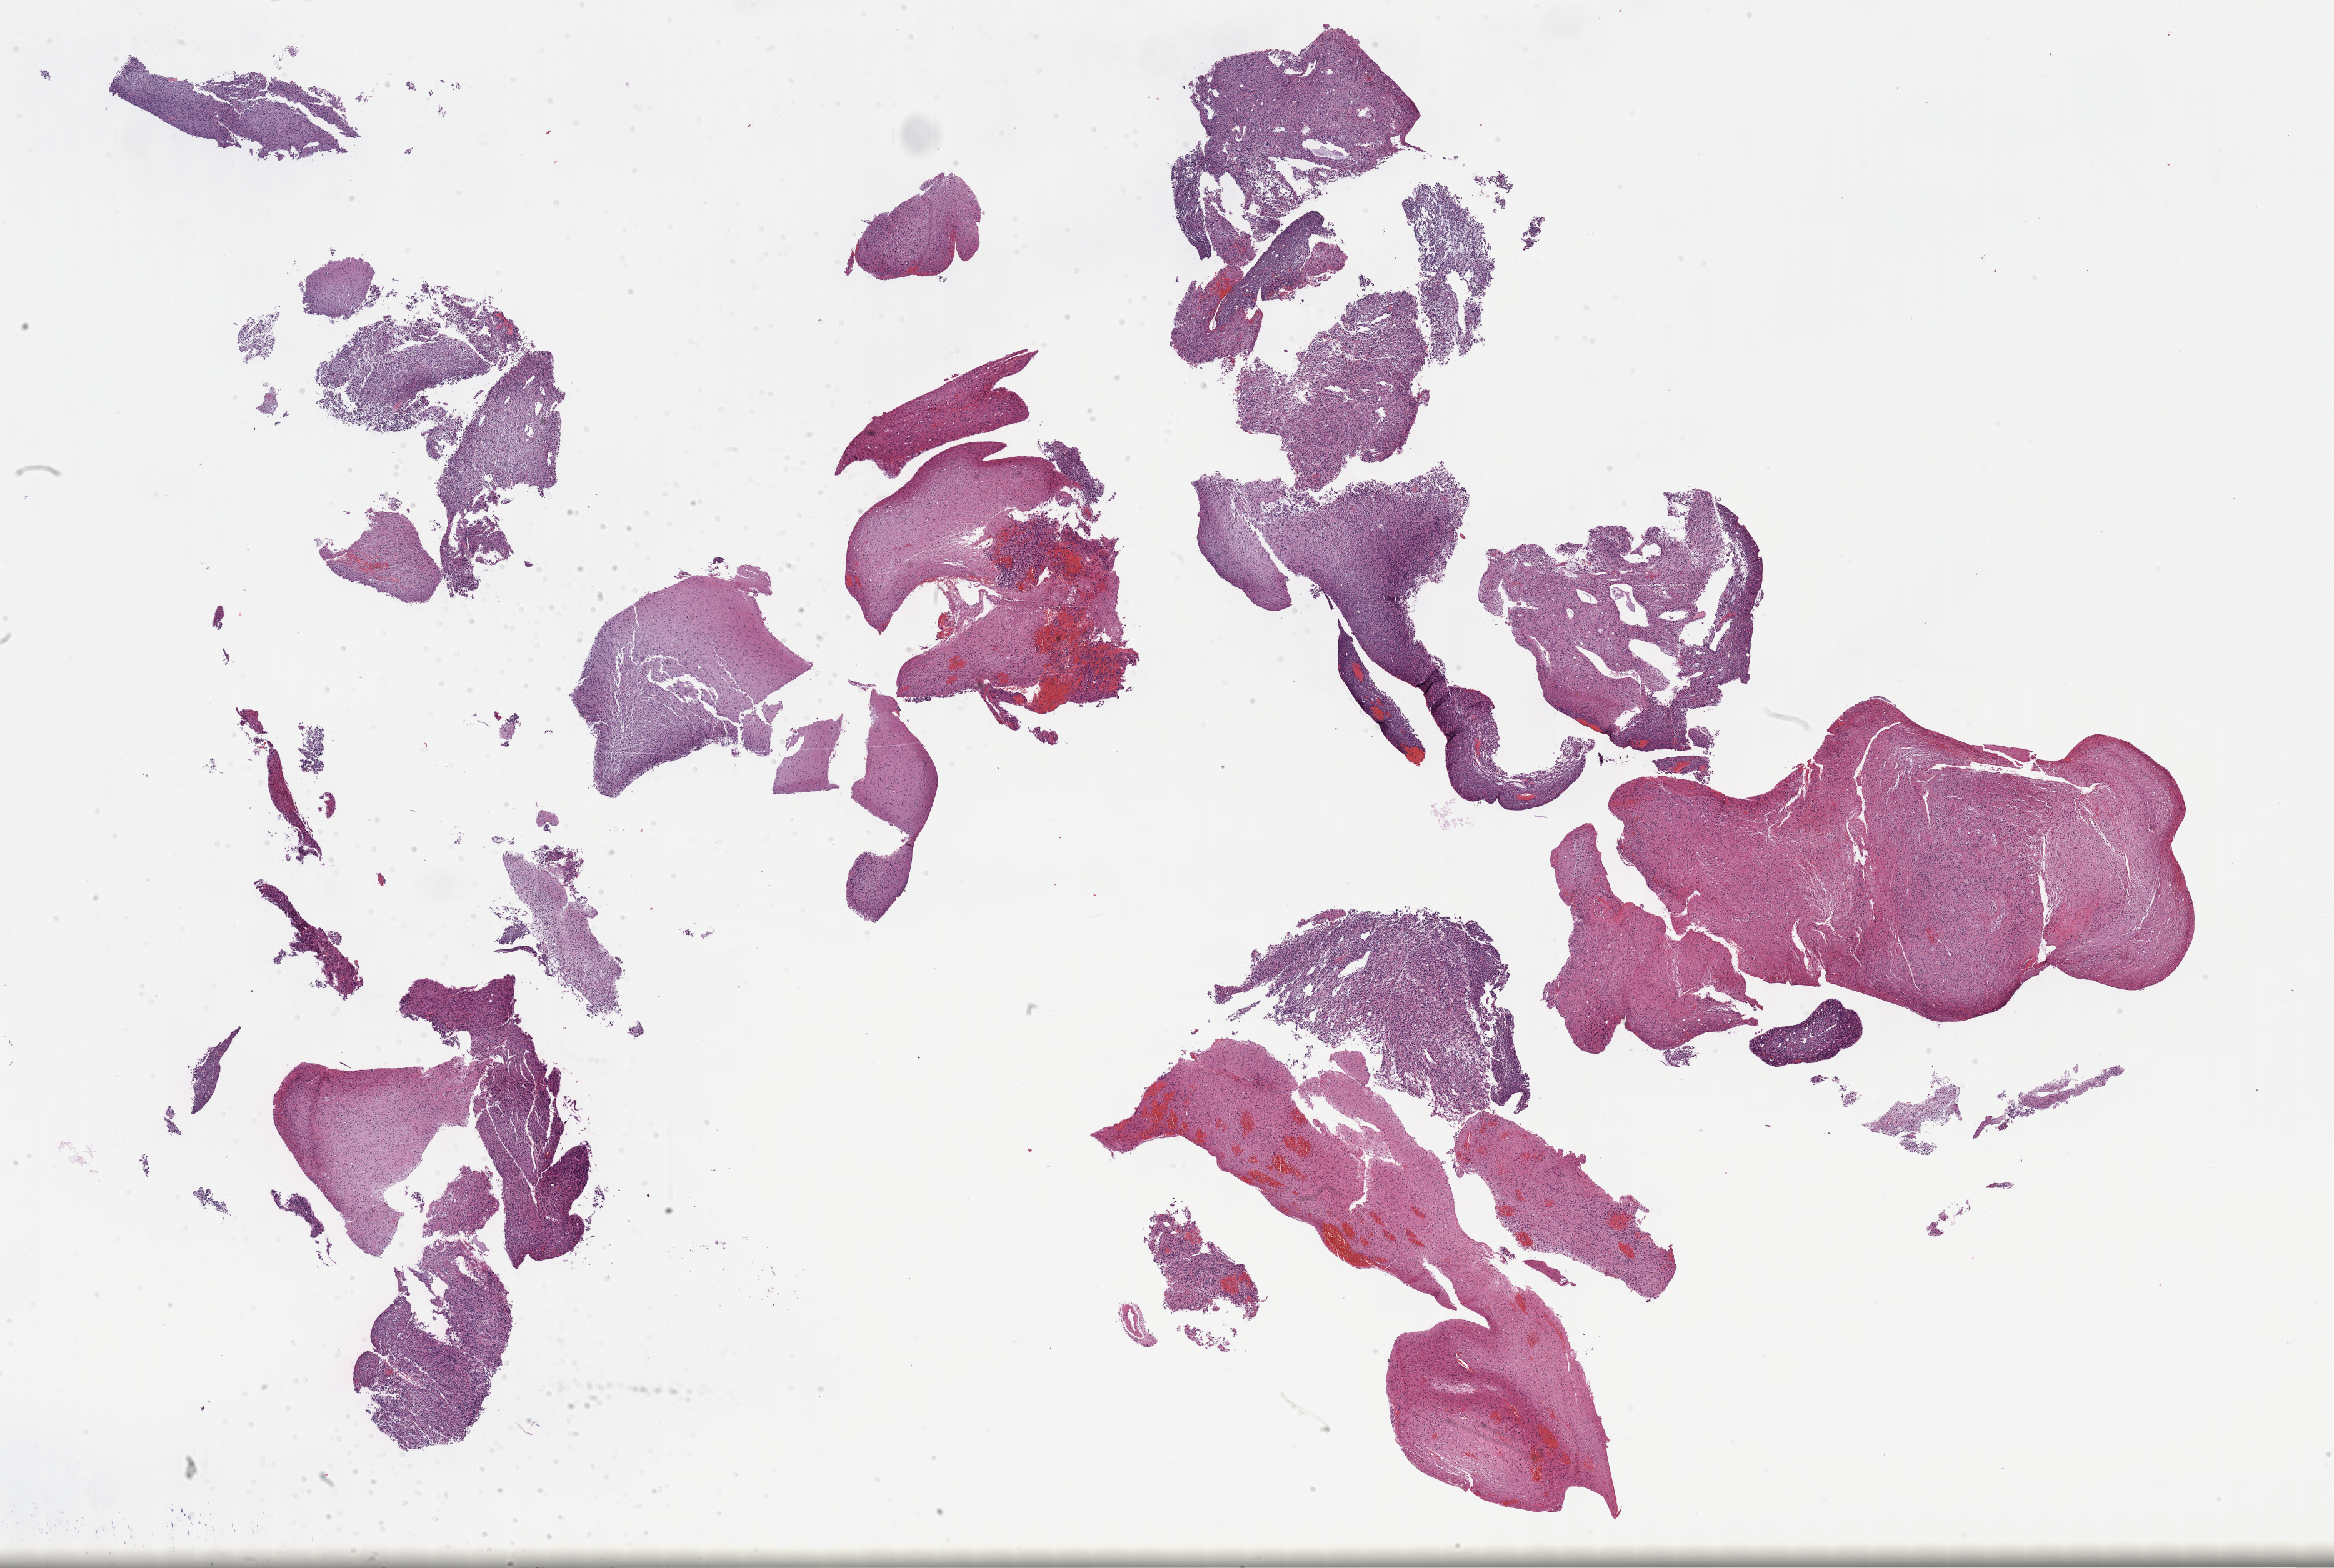
Whole-slide histology image, Hematoxylin and eosin (H&E) stained — shown as a low-resolution overview of the whole scanned area (about 30.2 x 20.3 mm), formalin-fixed paraffin-embedded (FFPE) diagnostic section, brain, primary tumour sample. Patient: female, age at initial diagnosis 44 years. Histologic grade: G3 (poorly differentiated).
Pathologic diagnosis: Astrocytoma, anaplastic (cerebrum).